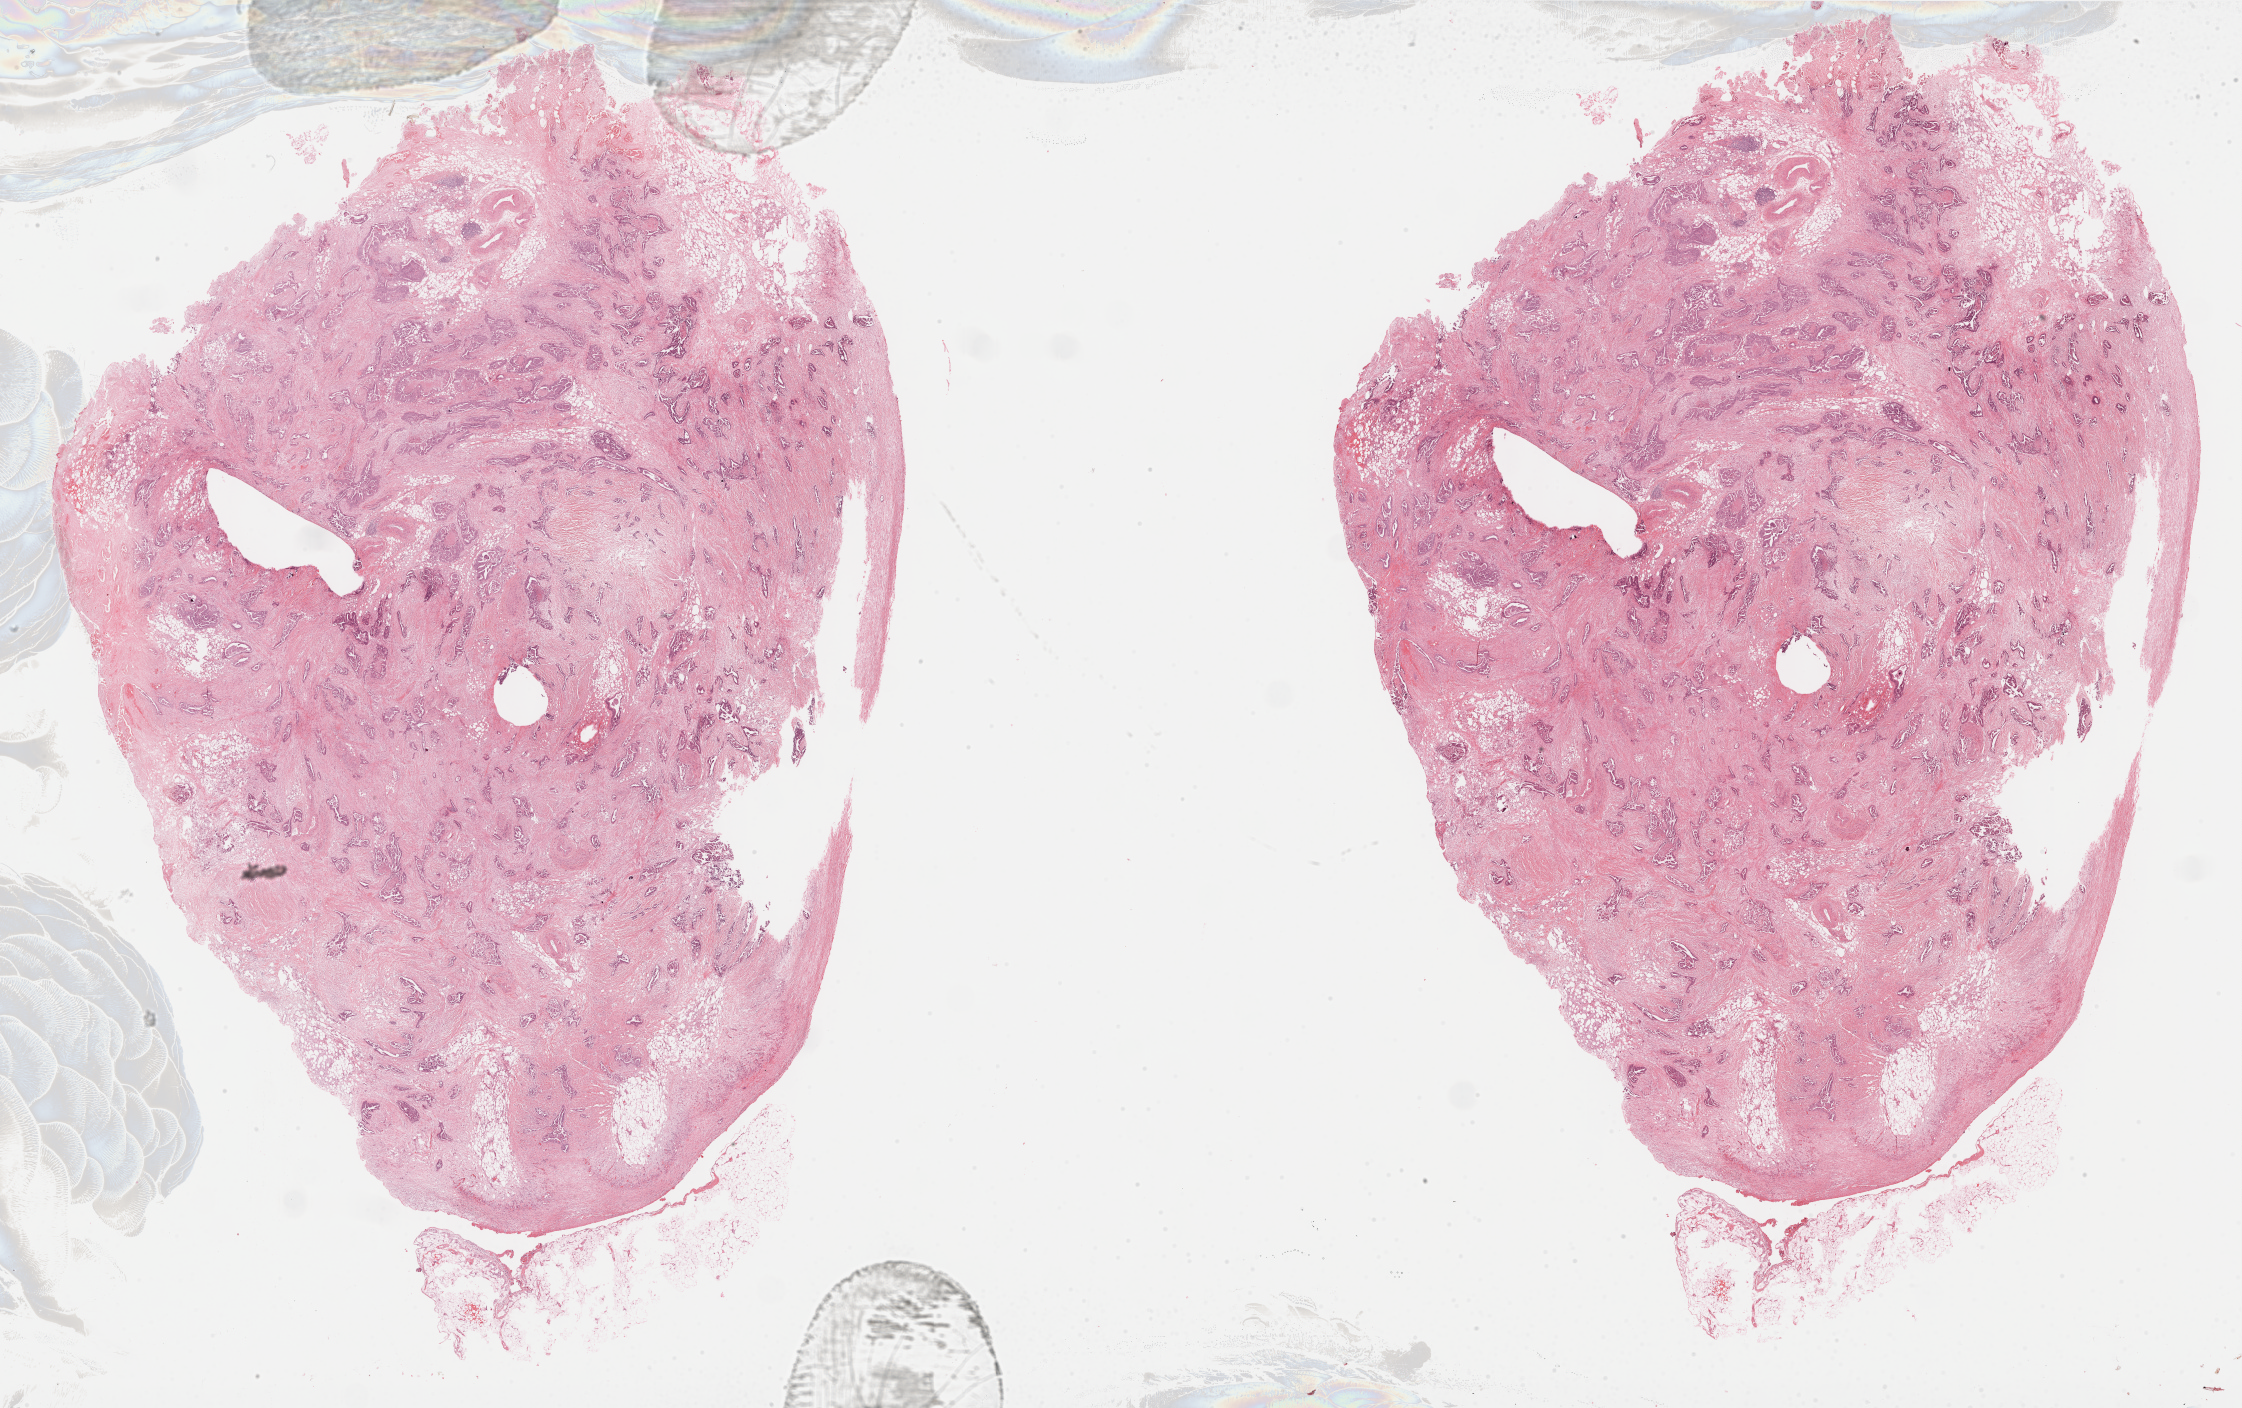
Whole-slide histology image, H&E, low-resolution overview of the scanned area, about 36.2 x 22.7 mm (slide scanned at 40x), formalin-fixed paraffin-embedded (FFPE) diagnostic section, sample: primary tumour, ovary. Female, age 73 years at initial diagnosis.
Pathologic diagnosis: Serous cystadenocarcinoma, NOS.